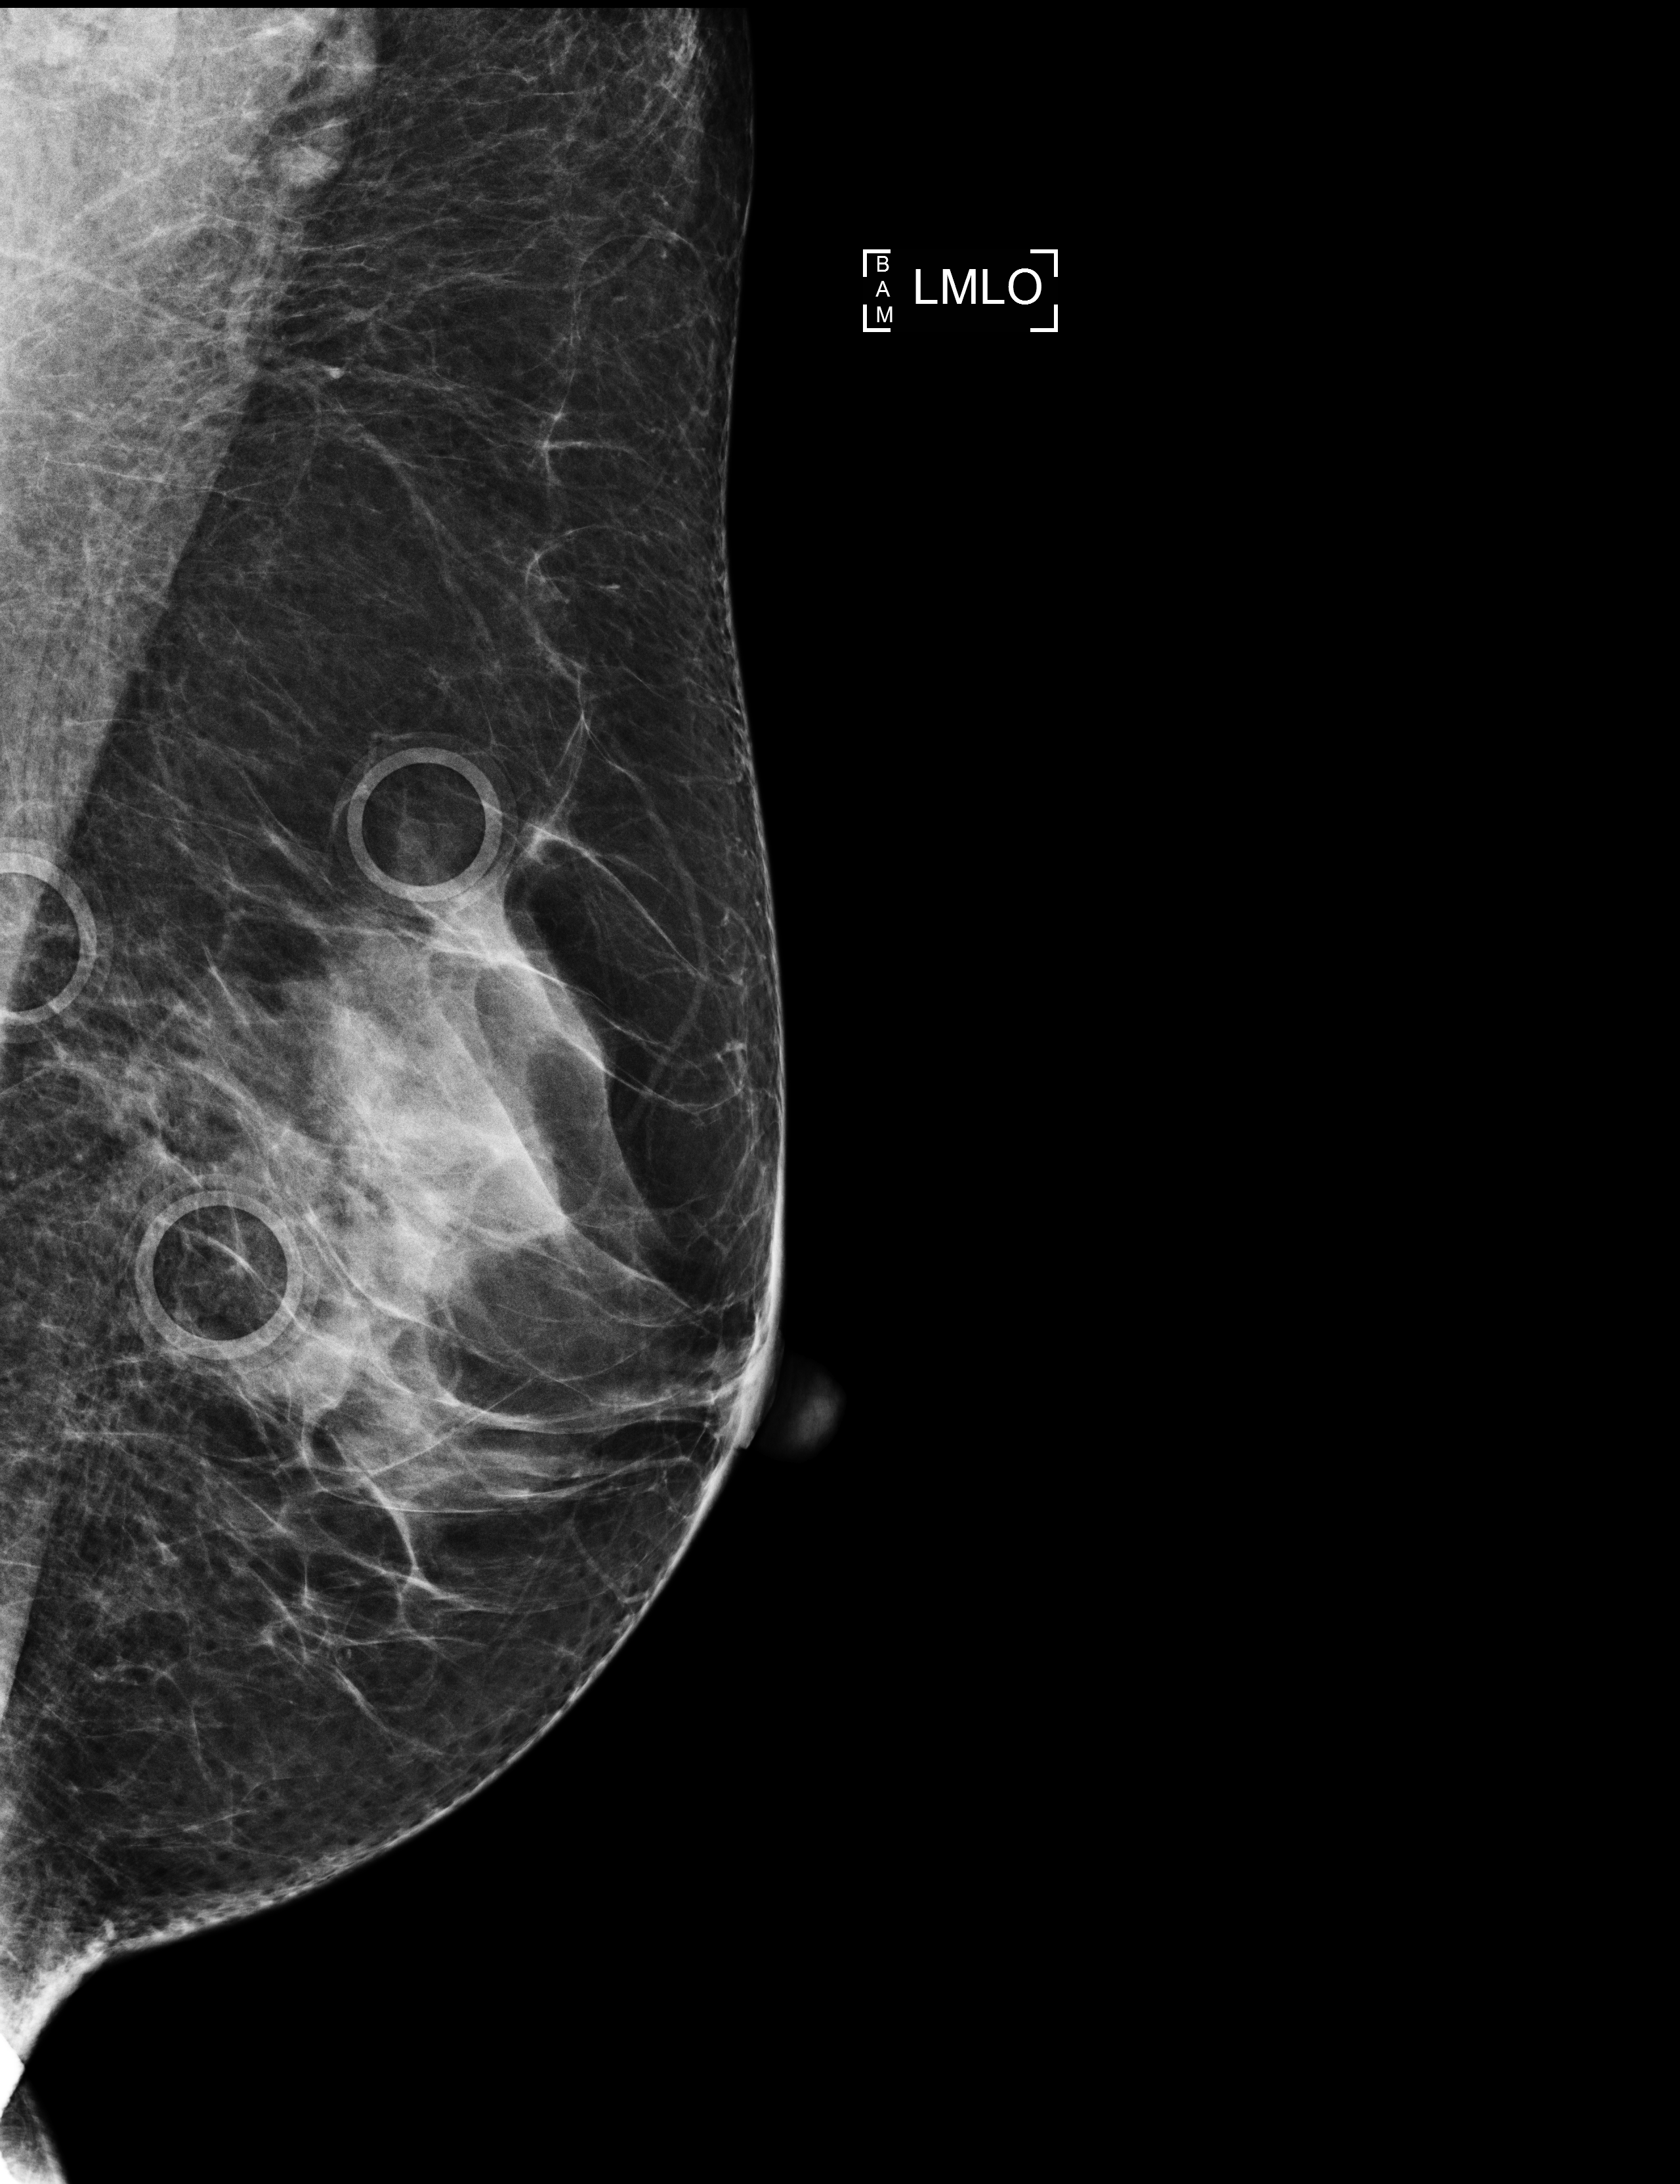
Screening examination, system: Selenia Dimensions. Patient aged 60 years (female).
Image type: full-field digital mammogram. Breast: left. Projection: MLO view.